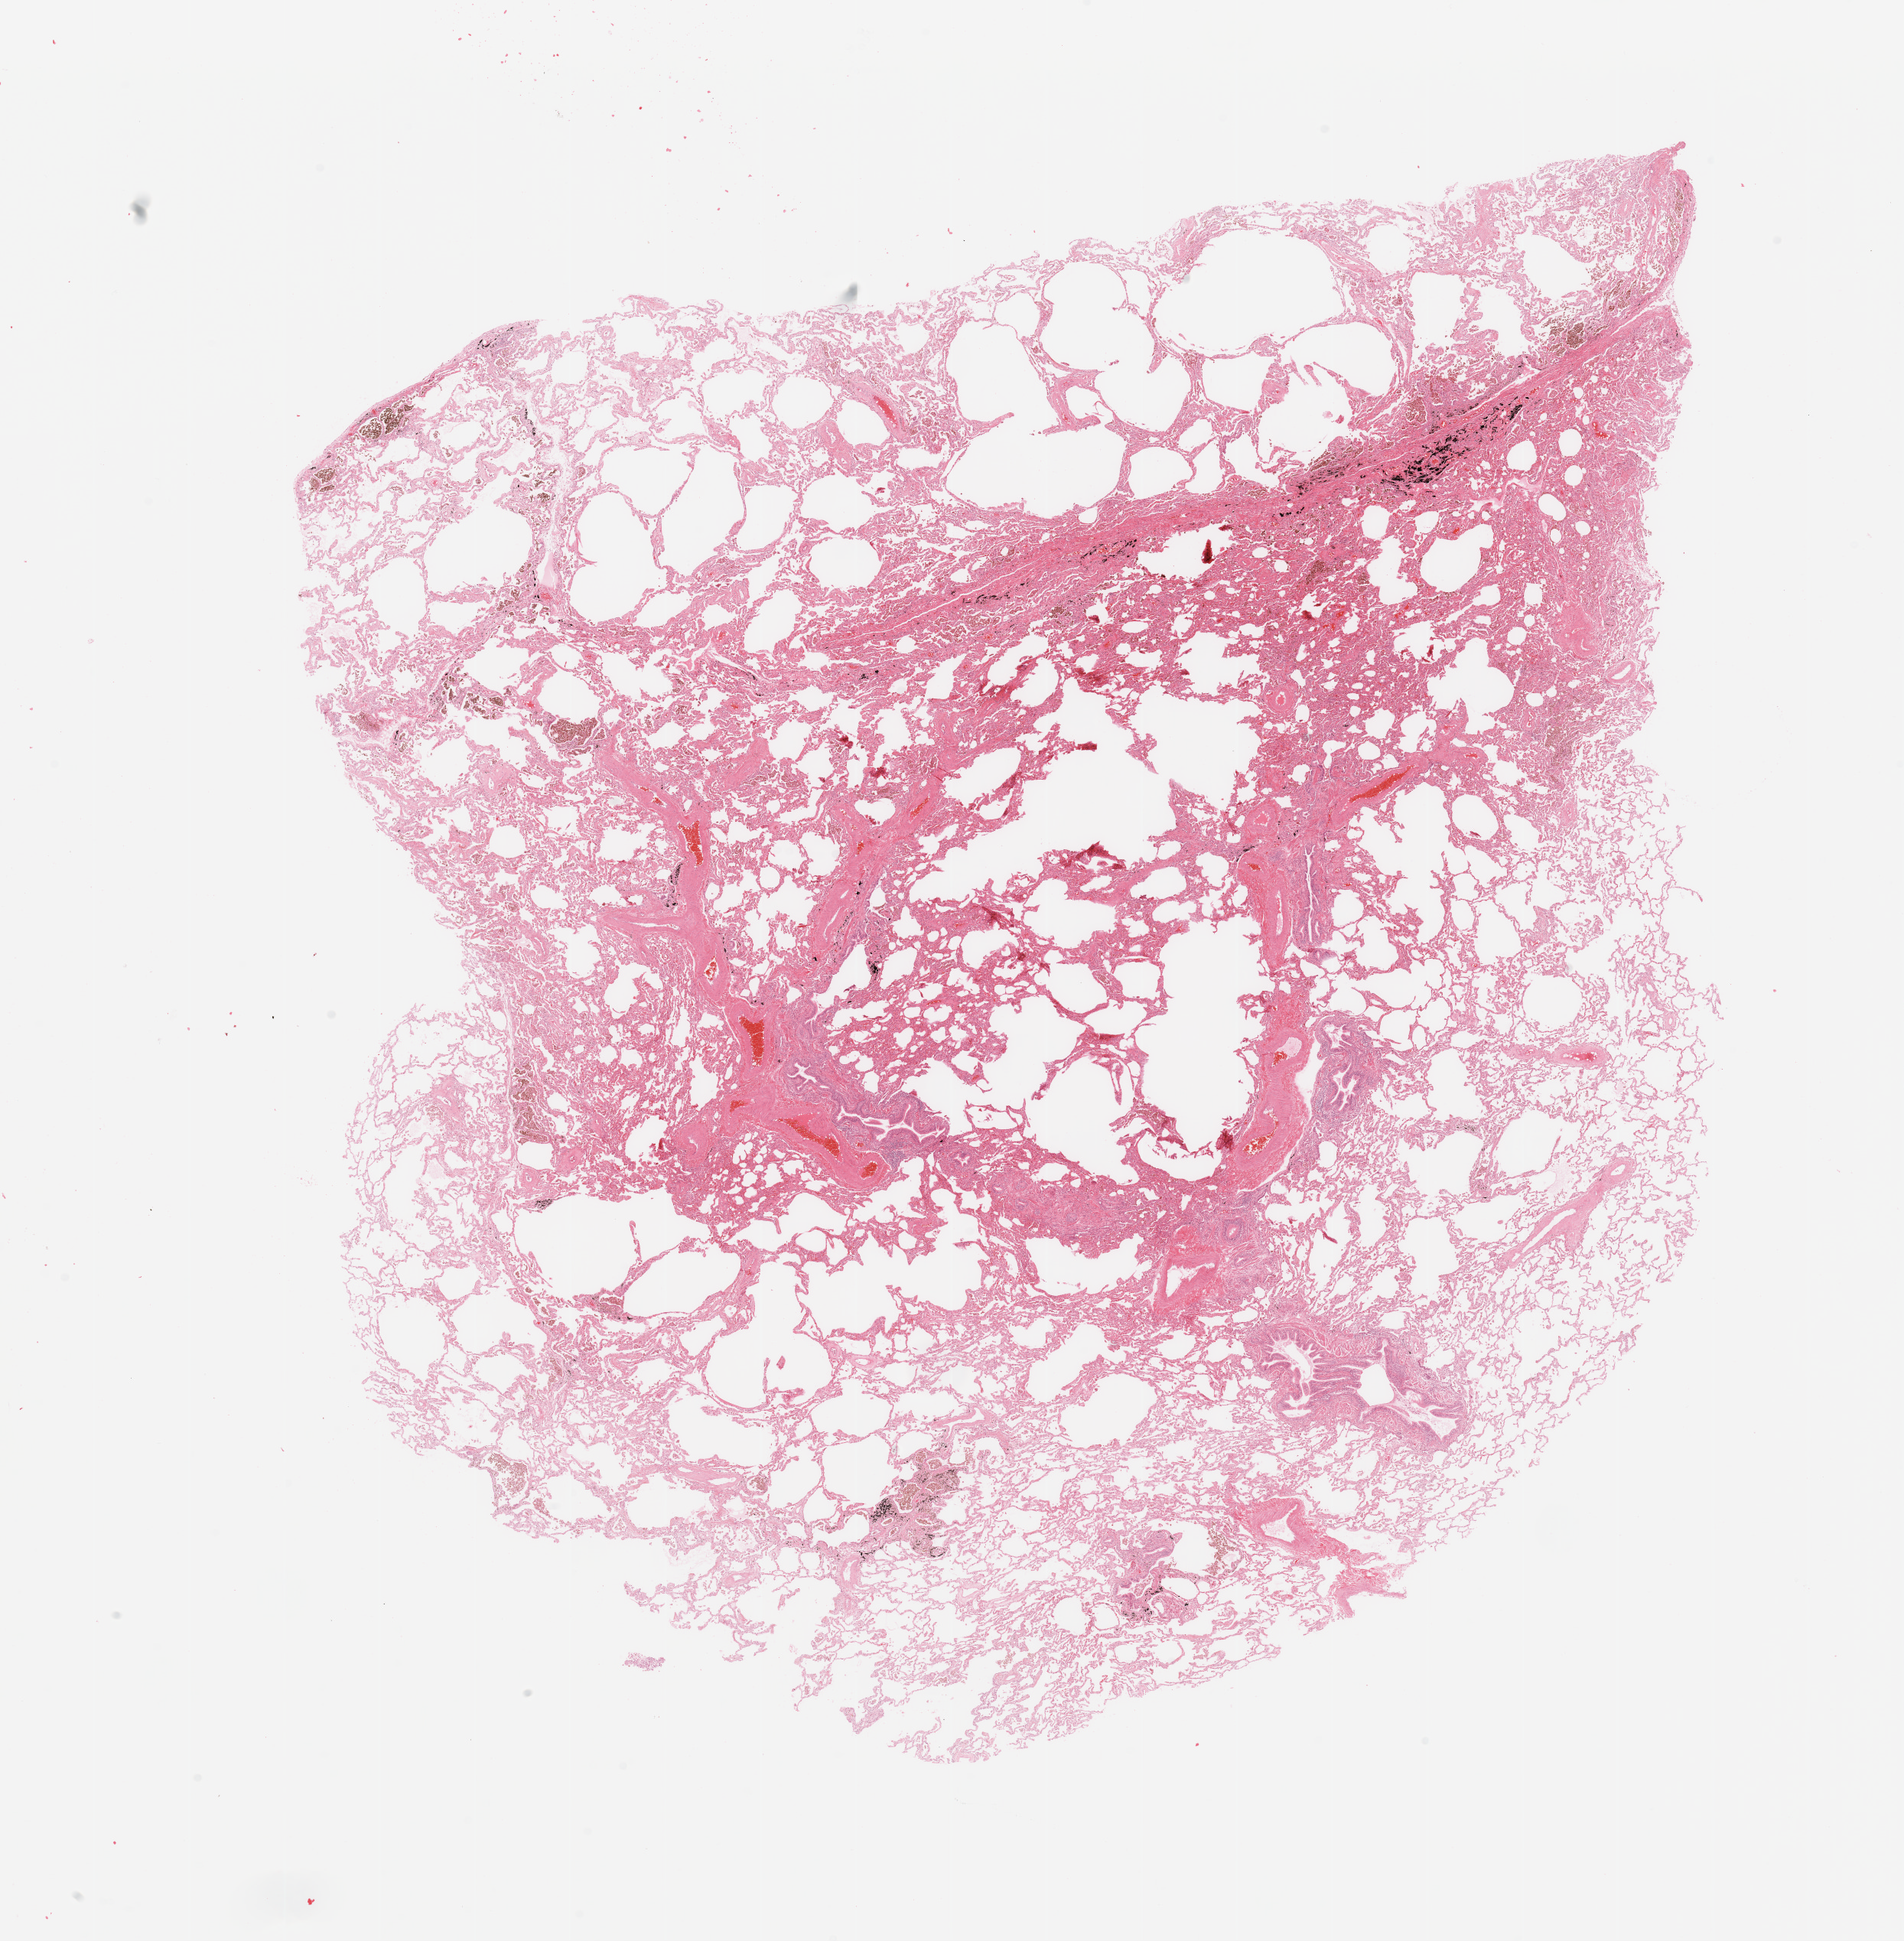
Whole-slide histology image, H&E, shown as a low-resolution overview of the whole scanned area (about 19.7 x 20.1 mm, from a 20x scan); normal (non-tumour) tissue sample, sampled site: lung. Patient: male, age 59 years.
This section: normal (non-tumour) tissue from the same patient. Patient diagnosis: Squamous cell carcinoma, NOS.